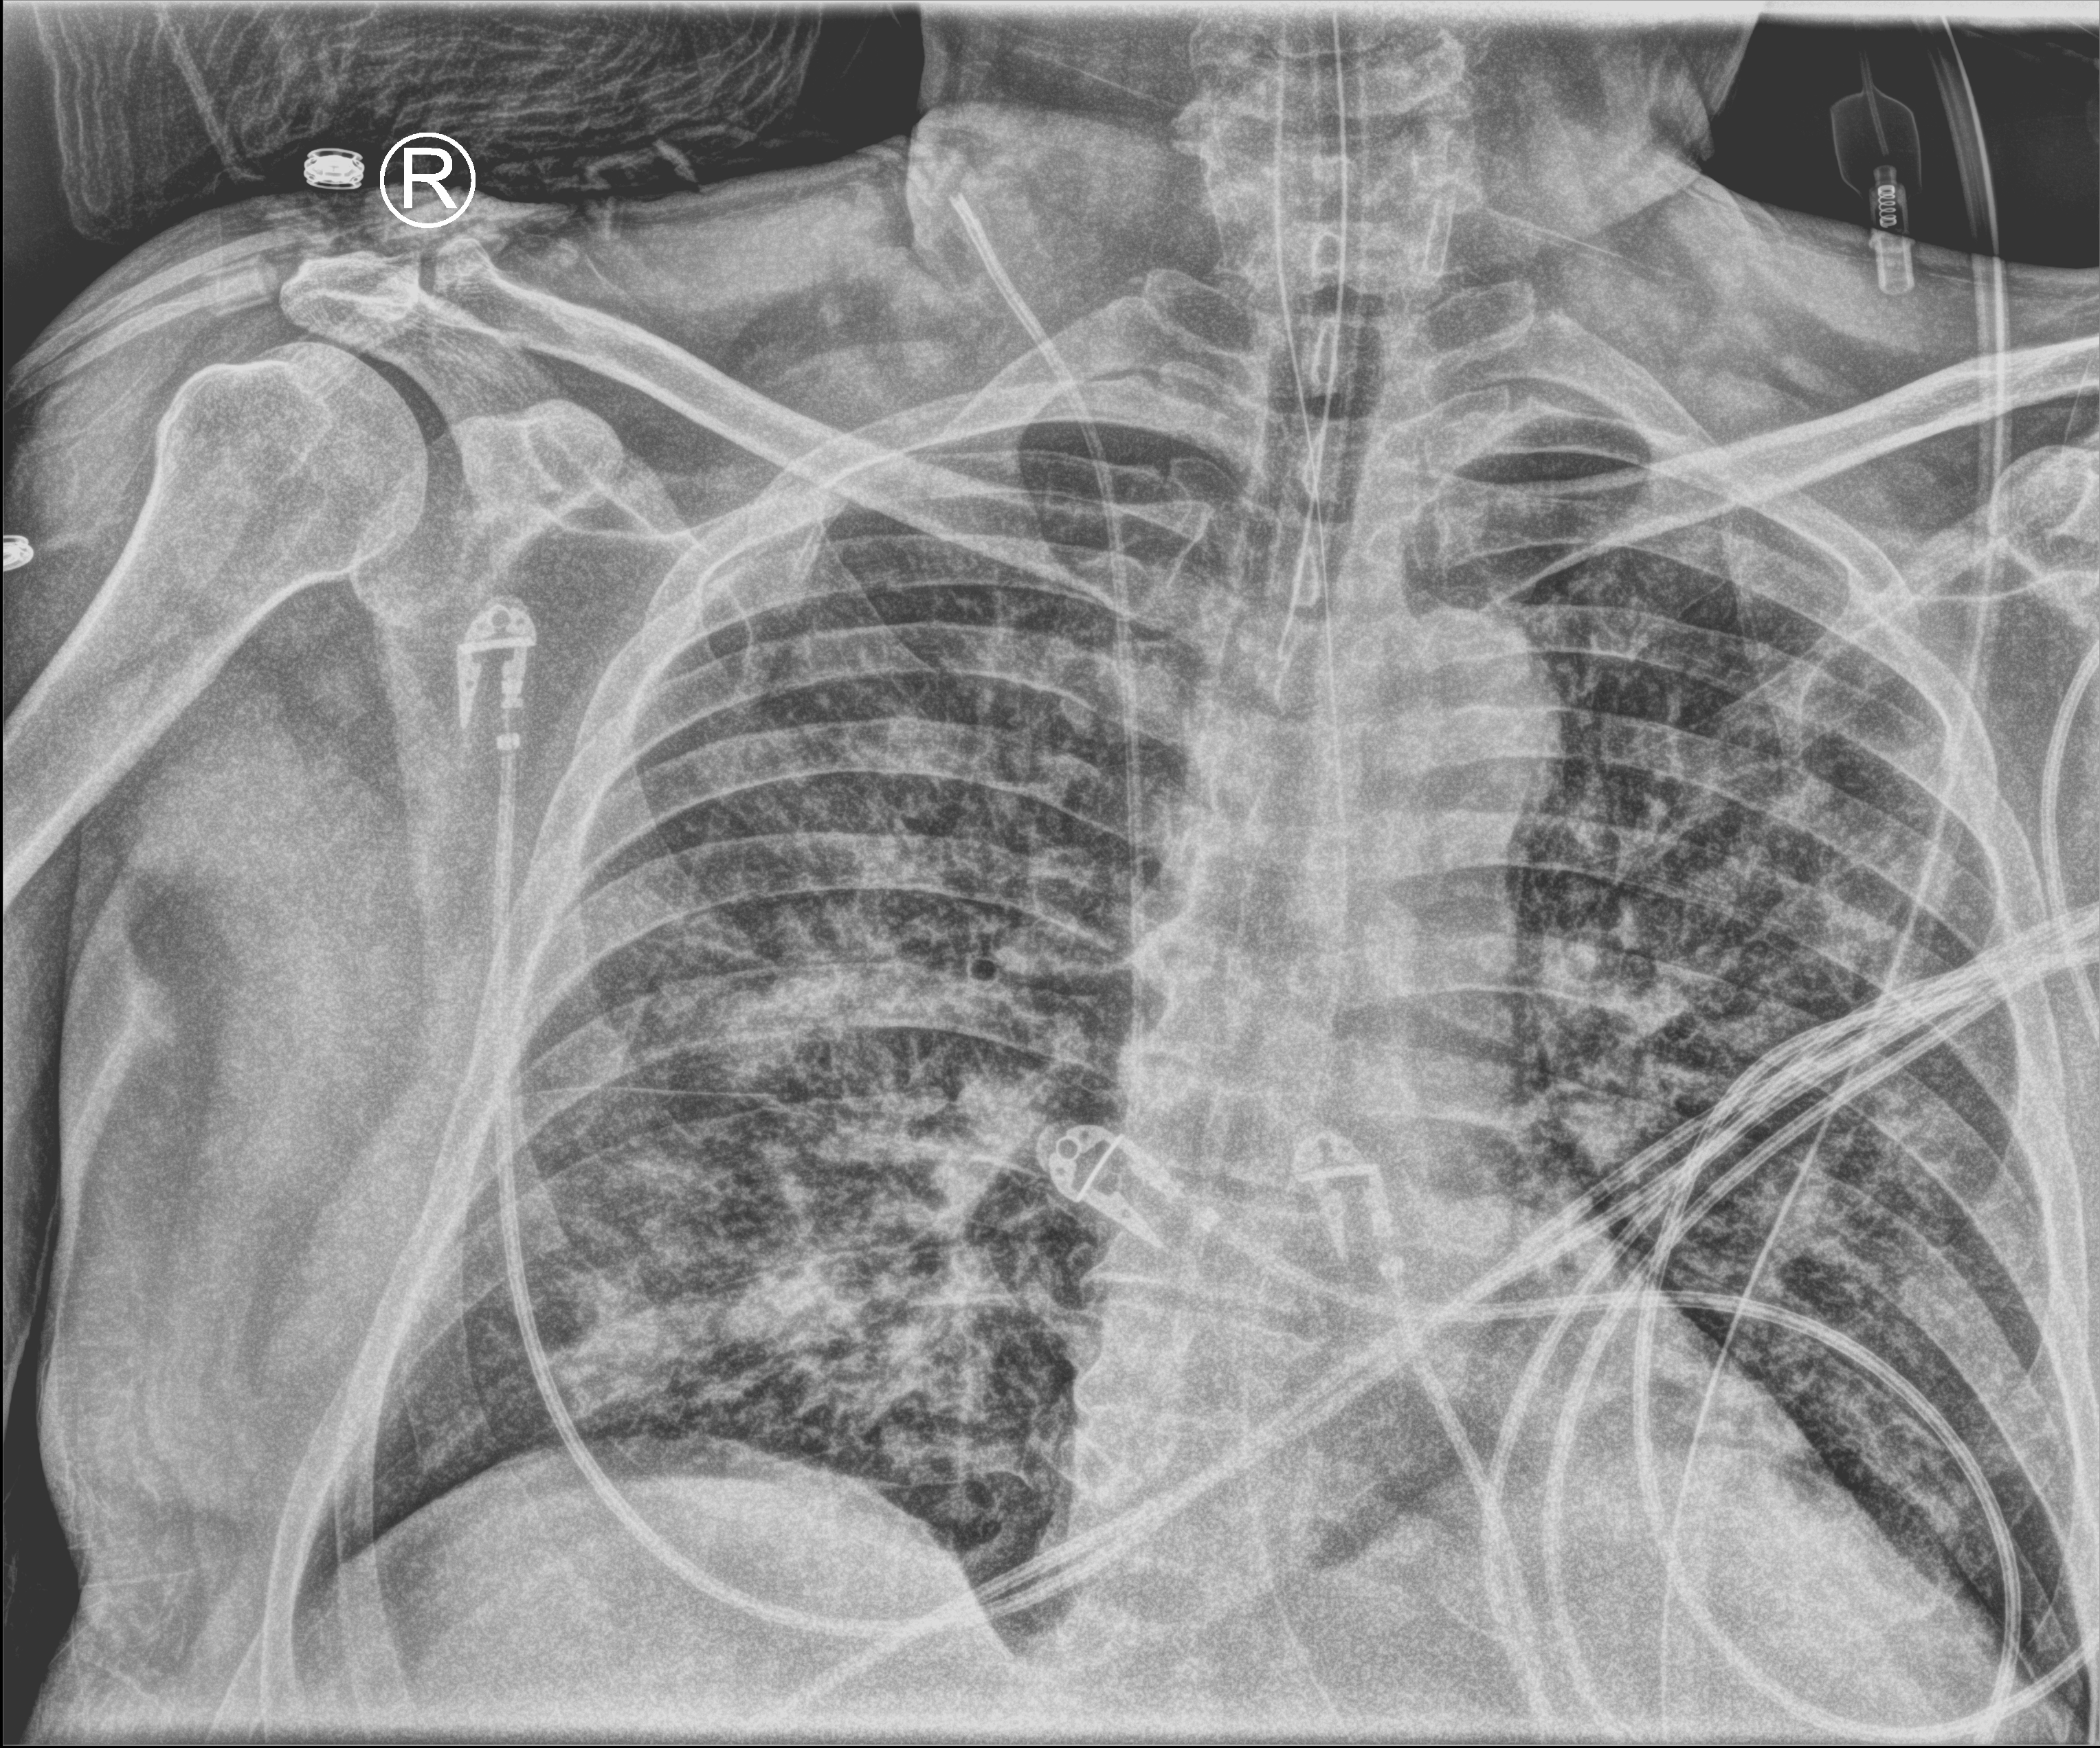
Chest X-ray (portable), anteroposterior (AP) projection. Male patient hospitalised with COVID-19, age 60–74 years.
From the hospital-stay record, not from the radiograph (when in the stay this image was taken is not recorded): hypertension (admission record): yes; other chronic lung disease (admission record): yes.